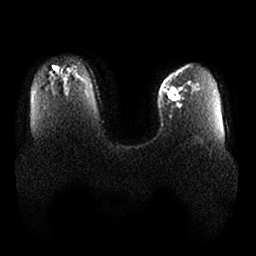
Breast MRI, one axial slice; position 21 of 25 along the scan axis; diffusion-weighted series; image 2 of 4 stored at this slice position (different b-values; order by instance number); 1.5 T; 4 mm slice thickness; 256 × 256 image matrix, field of view 380 × 380 mm. Female patient.
Structures marked on this image (outlined manually by an expert reader):
- tumour on diffusion-weighted imaging: box from (x=165, y=88) to (x=180, y=103) px